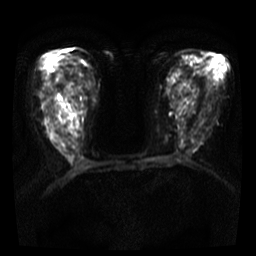
Breast MRI, one axial slice; slice 18 of 36 in the series (ordered by position); diffusion-weighted series; image 2 of 4 stored at this slice position (different b-values; order by instance number); 3 T; 5 mm slice thickness; 256 × 256 image matrix, field of view 300 × 300 mm. Female patient.
Annotated regions visible in this slice (expert manual segmentation):
- tumour on diffusion-weighted imaging: box from (x=56, y=143) to (x=65, y=155) px